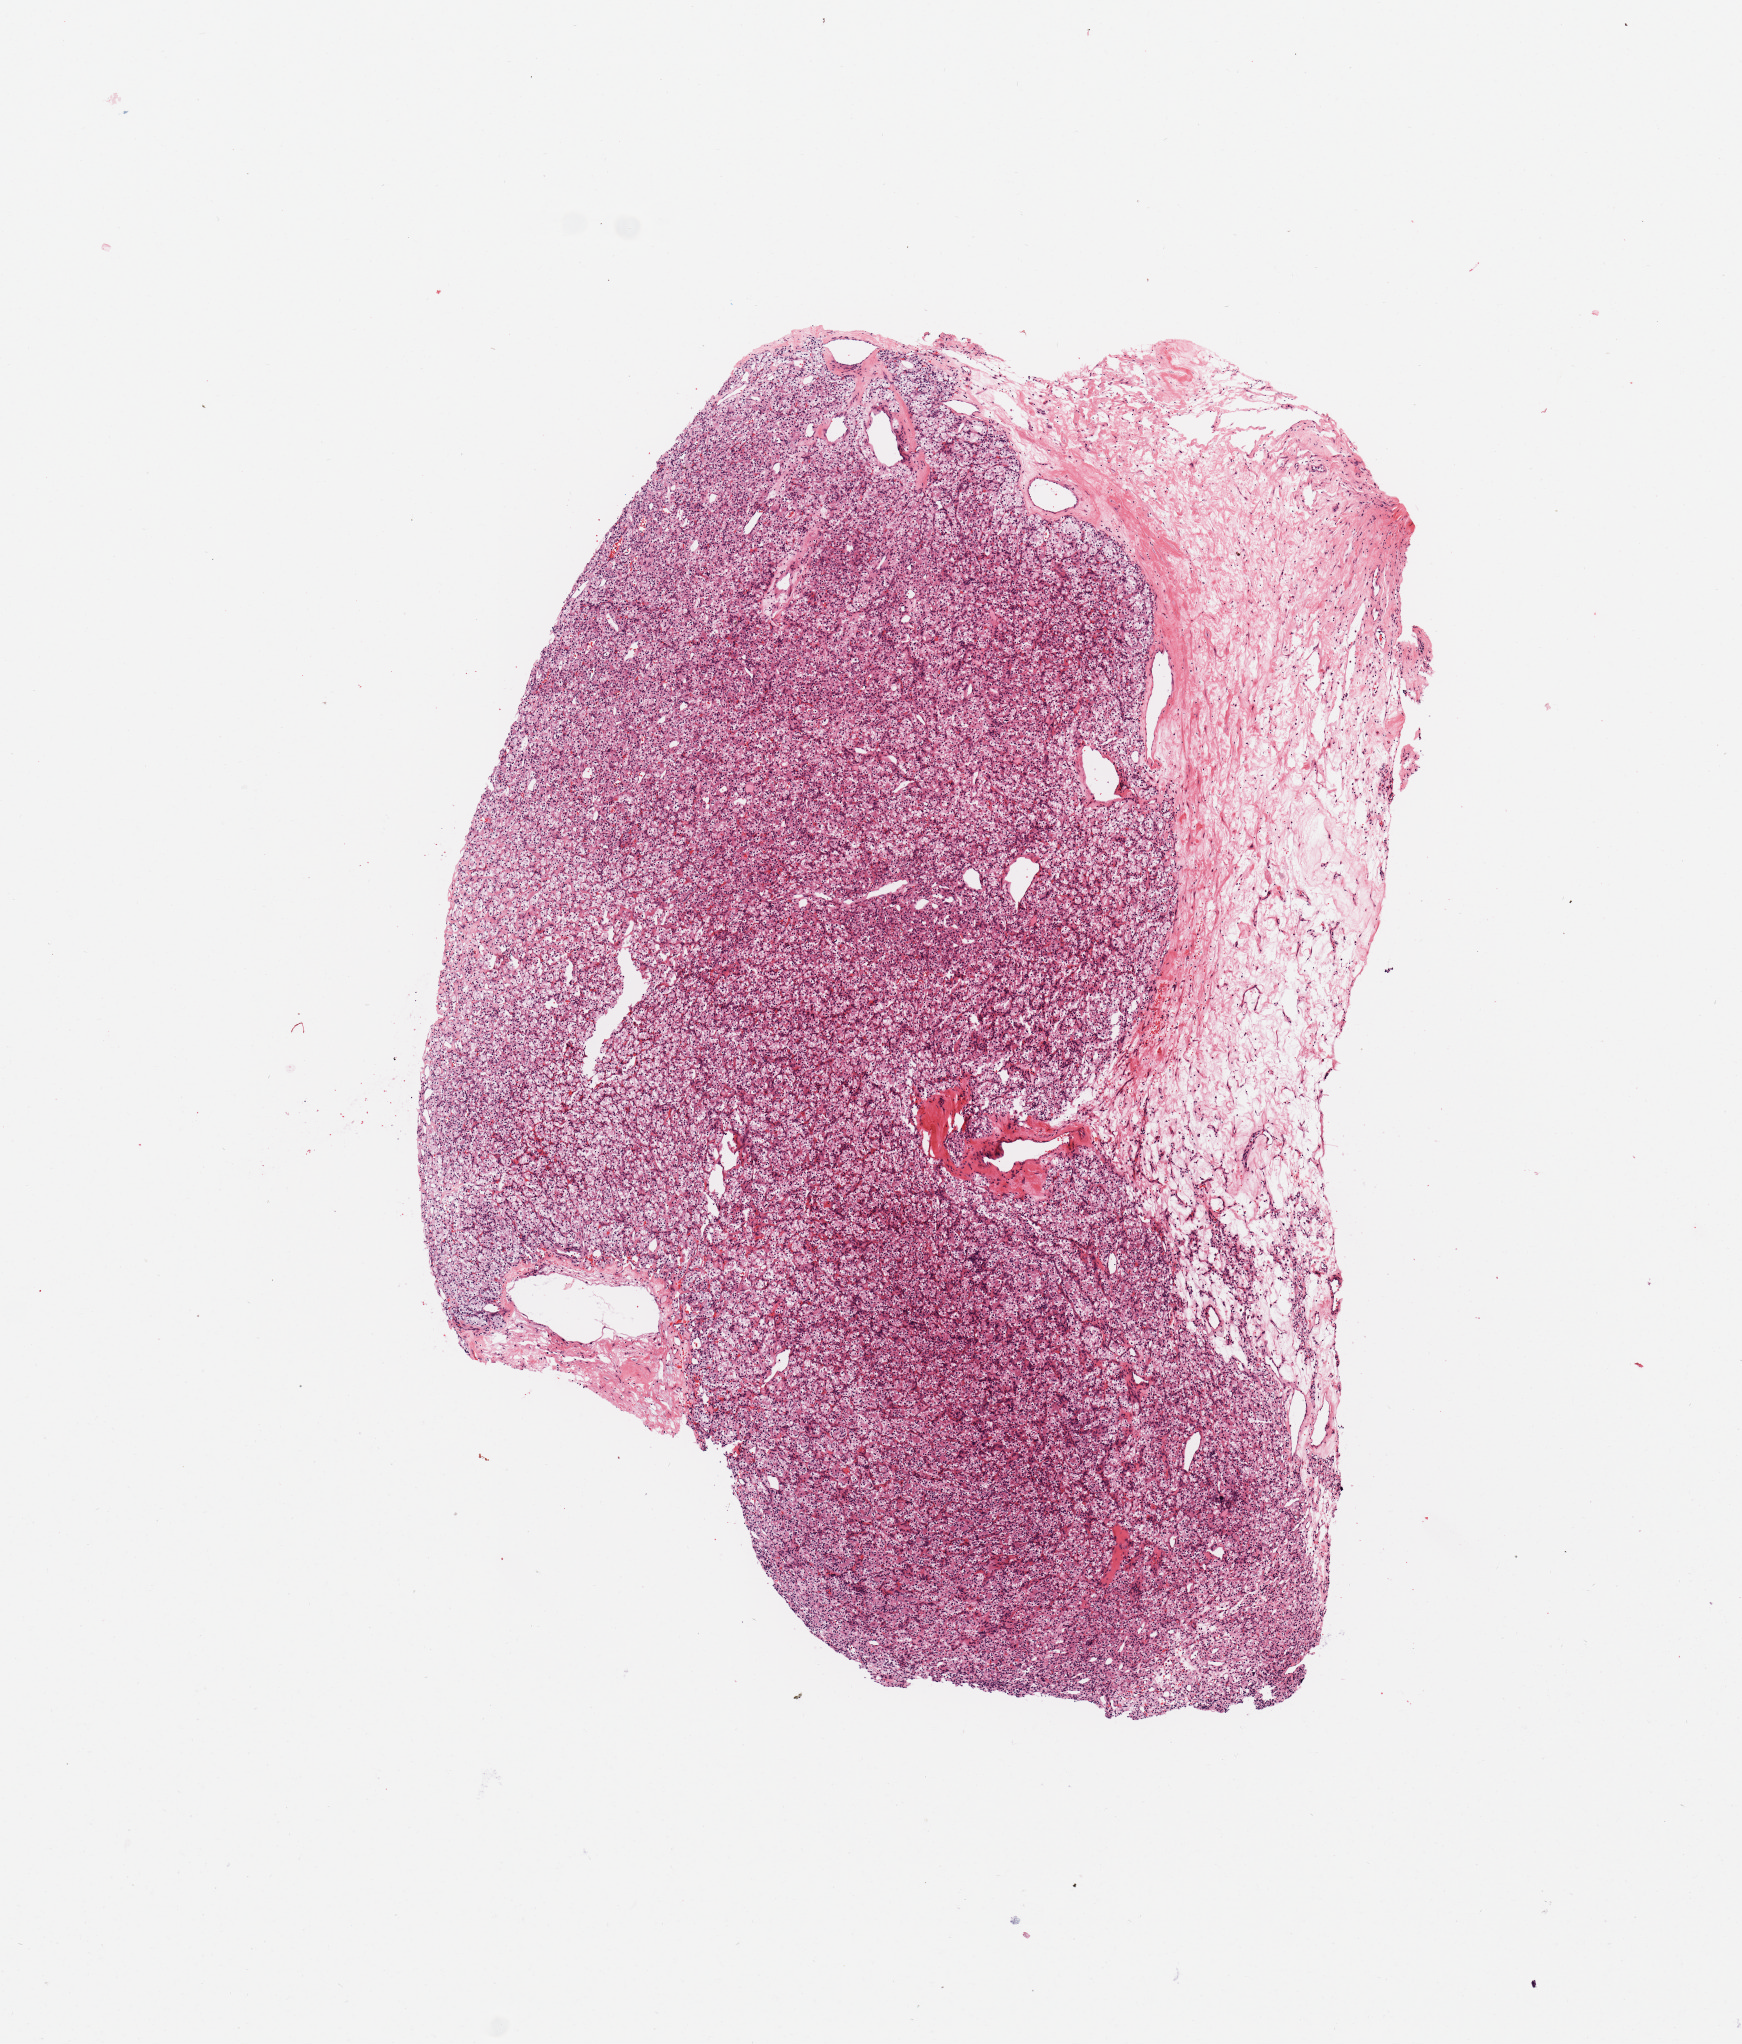
Whole-slide histology image, H&E-stained, whole scanned area (about 6.9 x 8.1 mm, slide scanned at 20x) shown as a low-resolution overview, tumour tissue sample, sampled site: kidney. 61-year-old female patient. Histologic grade: G2 (moderately differentiated). Composition of this section per pathologist review: tumour nuclei 80%, necrosis 8%.
* diagnosis: Renal cell carcinoma, NOS
* primary tumour site (as recorded): lower pole
* AJCC pathologic stage: II